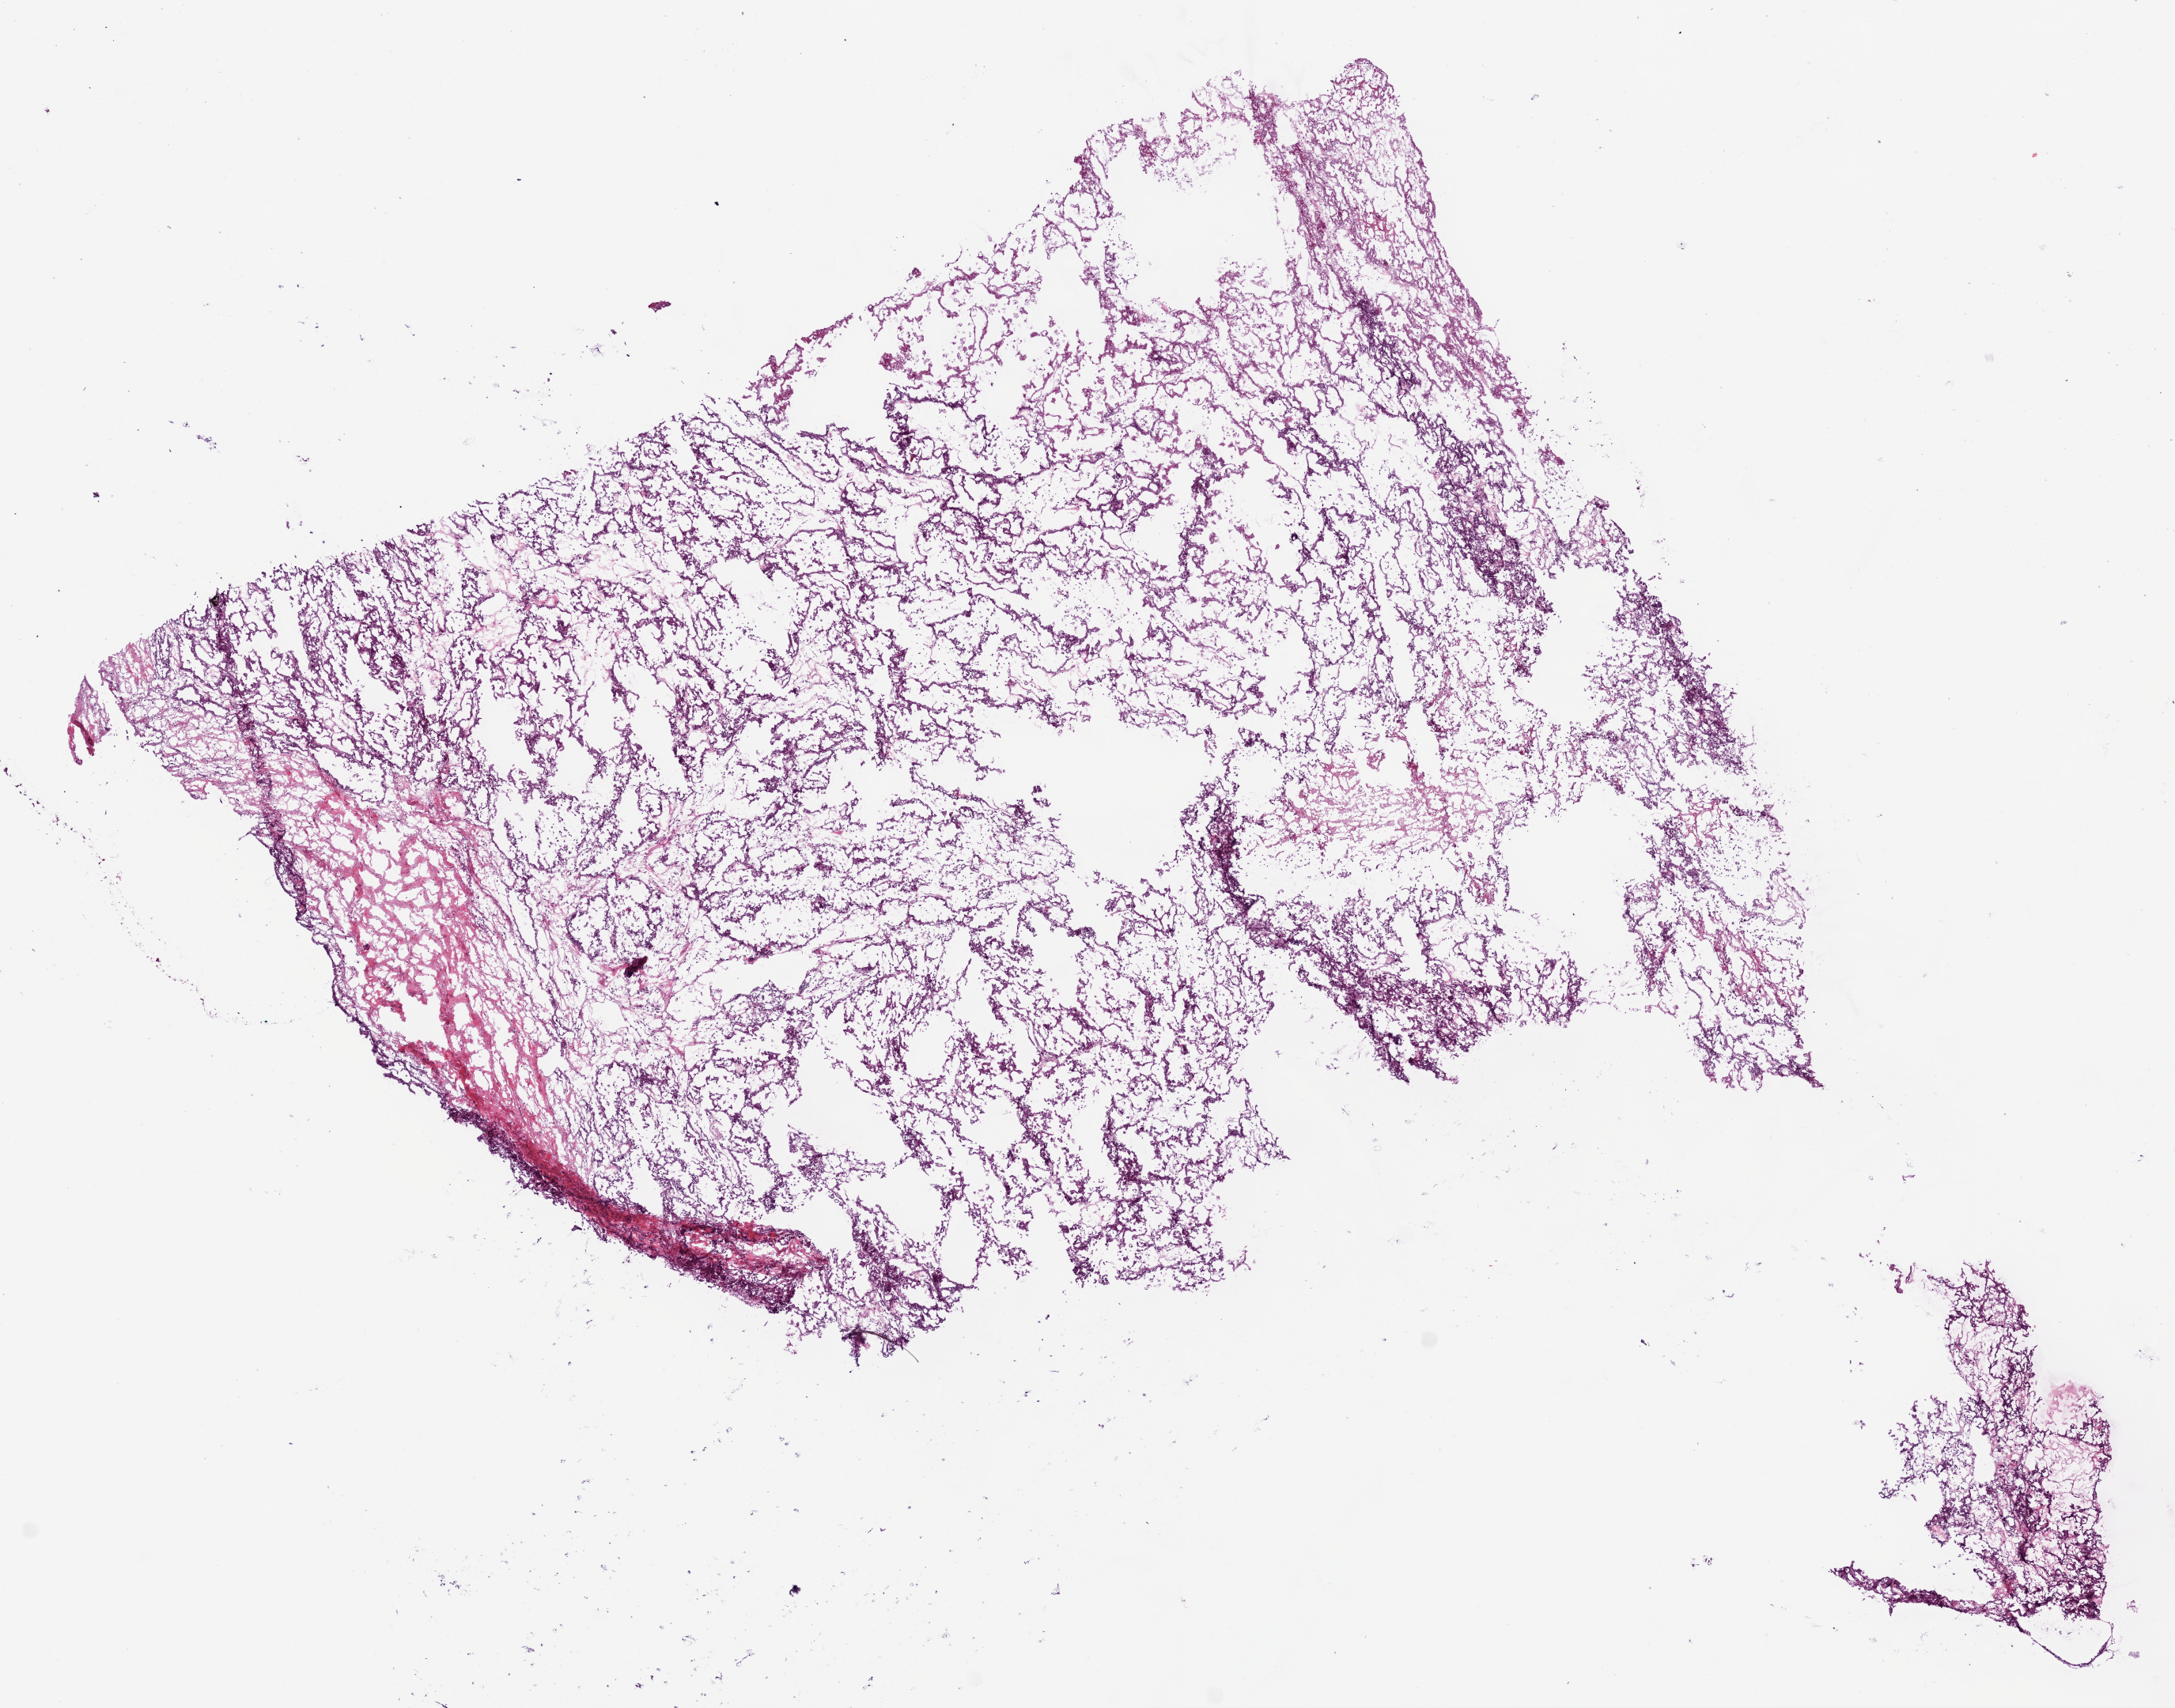
H&E whole-slide image — shown as a low-resolution overview of the whole scanned area (about 11.0 x 8.7 mm, acquisition: 20x scan). Frozen section. Sample: primary tumour, kidney. Male patient; age at initial diagnosis 55 years. Slide review estimates, as recorded: tumour cells 90%, tumour nuclei 80%, normal cells 0%, stromal cells 5%, necrosis 5%.
• lymph nodes positive (case pathology): 0 of 33 examined
• pathologic diagnosis: Papillary adenocarcinoma, NOS
• AJCC pathologic stage: II (6th edition)
• laterality: left